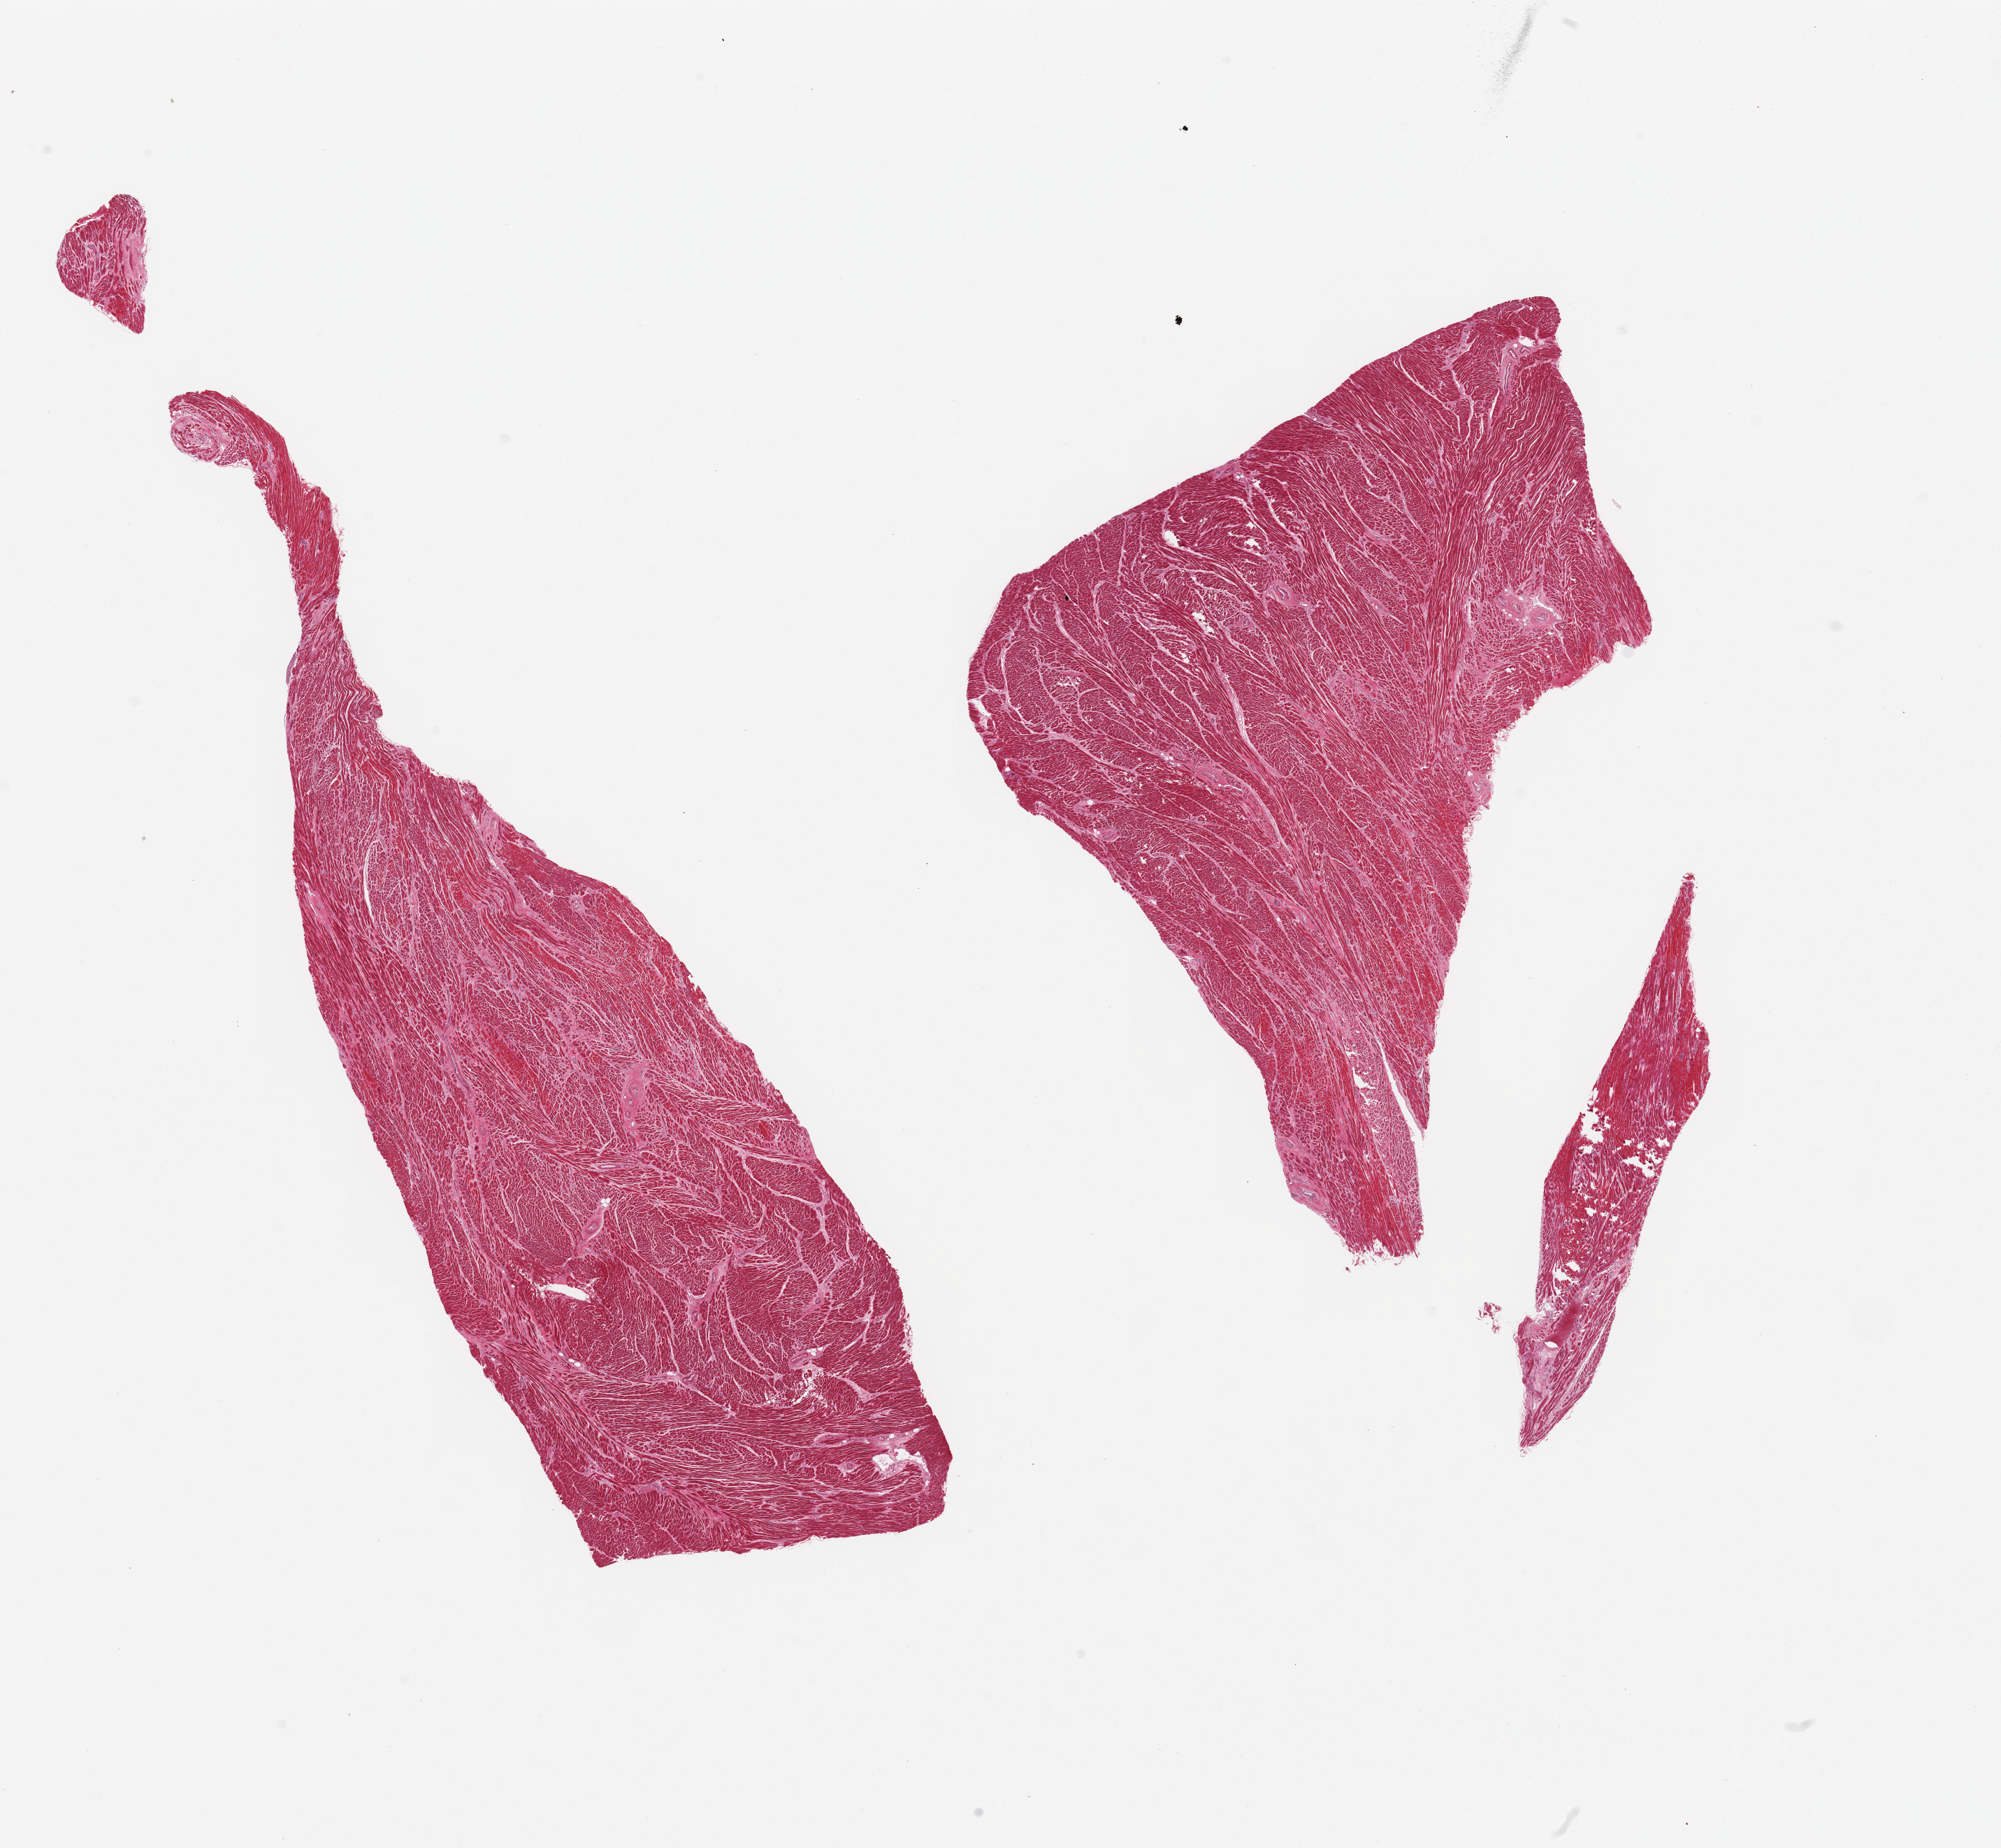
Digitized haematoxylin and eosin-stained section, brightfield — whole scanned area (about 22.6 x 20.9 mm) shown as a low-resolution overview, PAXgene-fixed, paraffin-embedded tissue, sampled site (target tissue): heart, tissue donor sample. Donor sex: male.
• pathologist's review note for this sample: 2 pieces; foci of hypereosinophilic myofibers consistent with ischemia